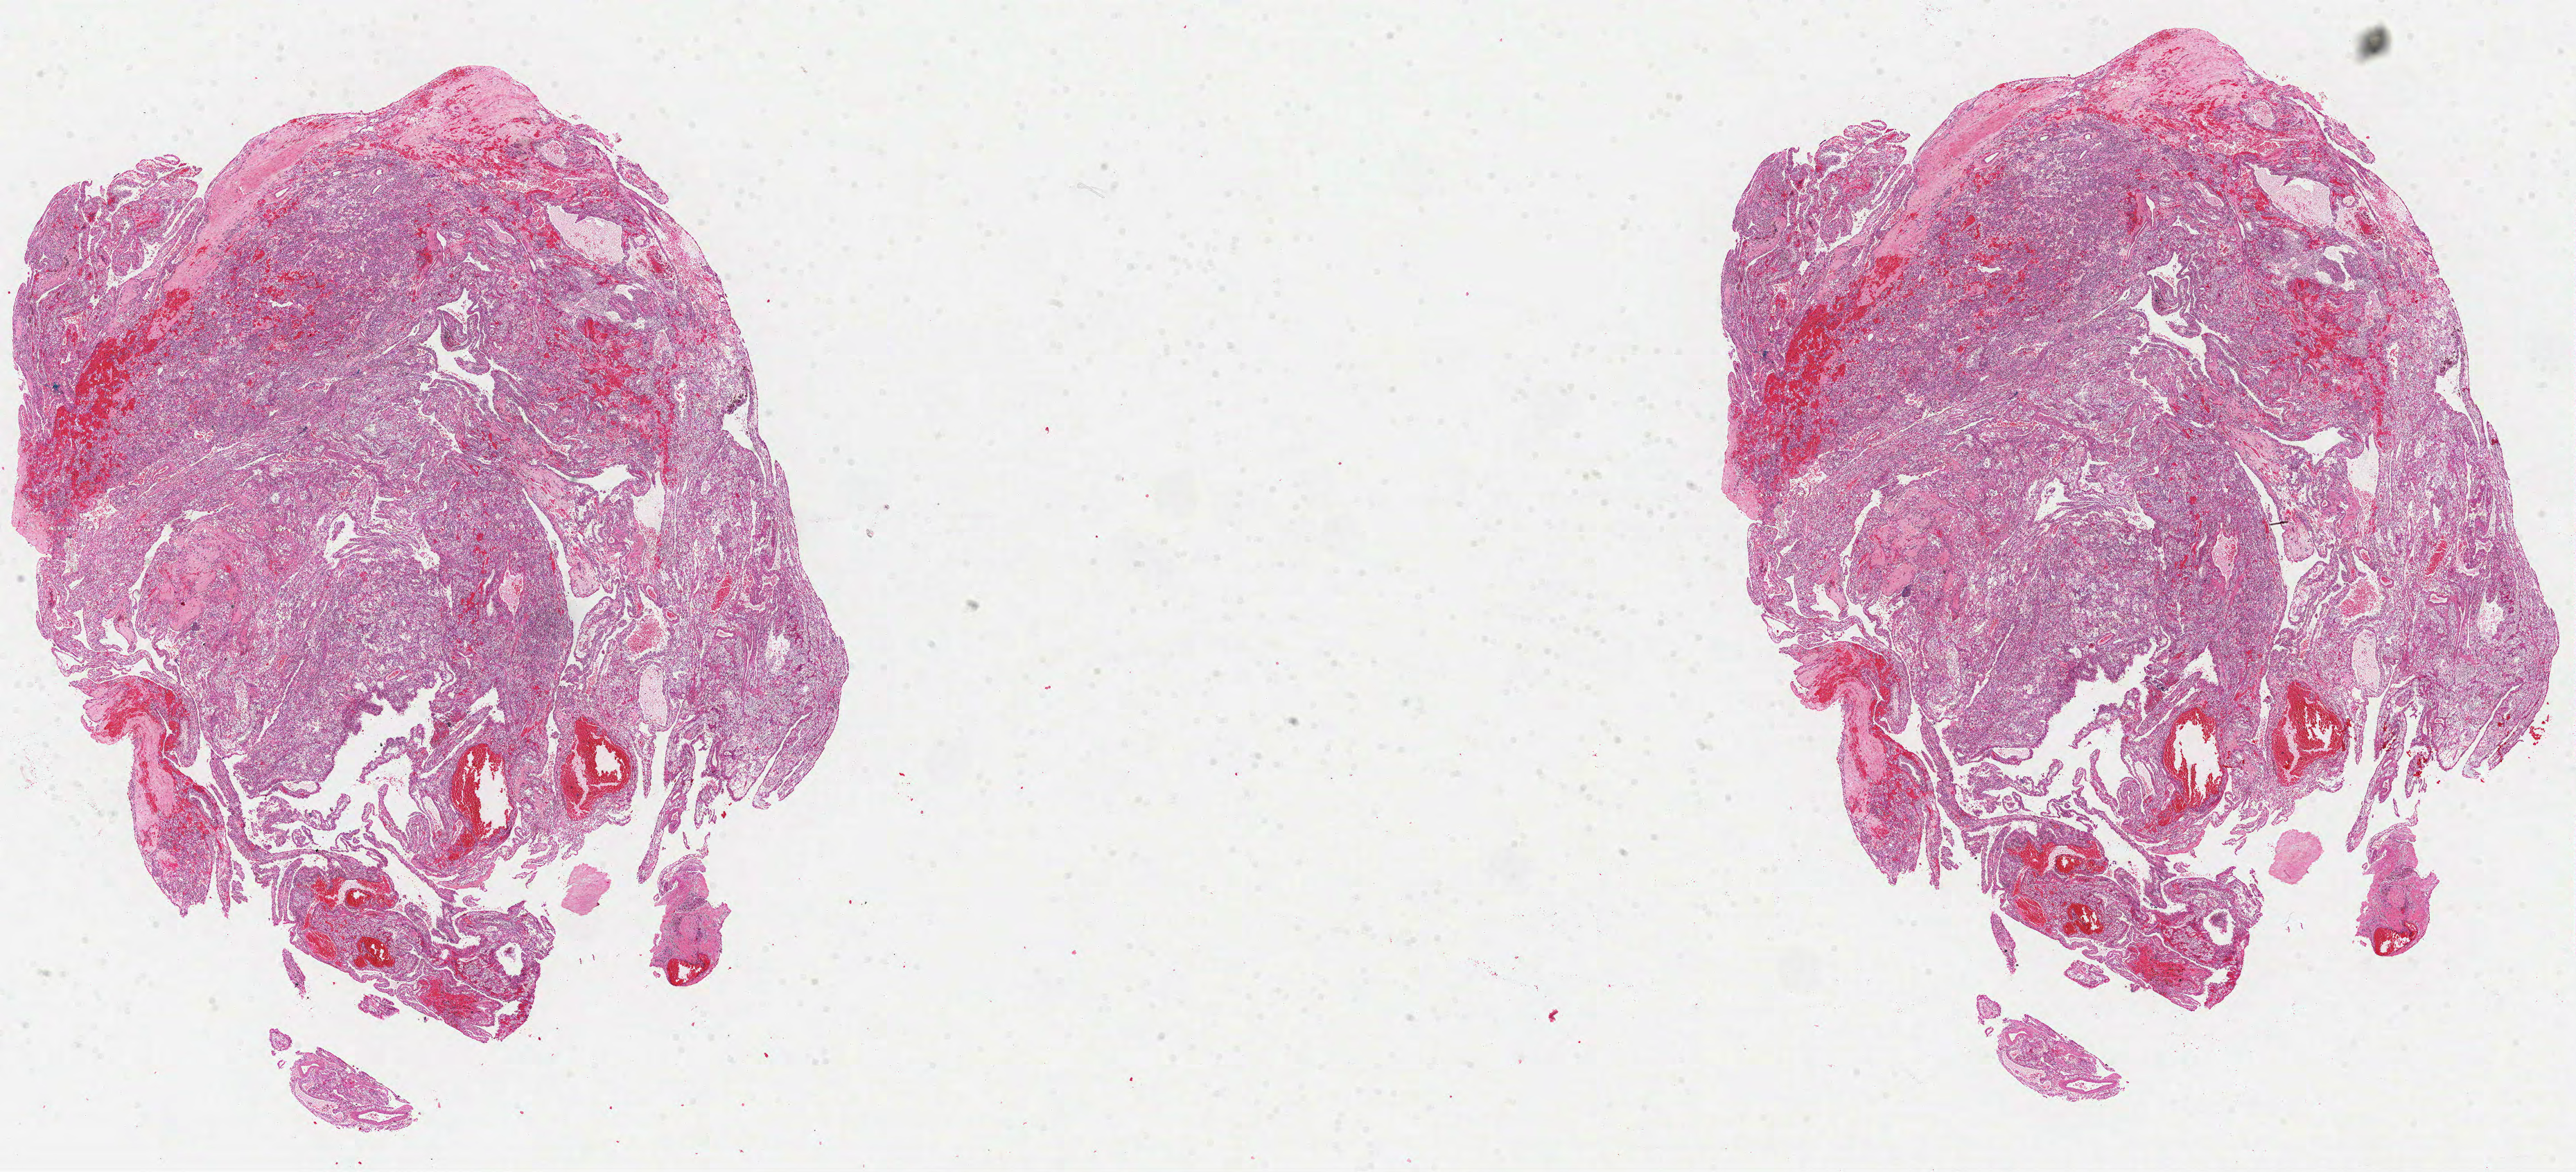
Digitized Hematoxylin and eosin (H&E) stained tissue section (whole slide) — whole scanned area (about 30.0 x 13.6 mm, from a 40x scan) shown as a low-resolution overview, formalin-fixed paraffin-embedded (FFPE) diagnostic section, sample: primary tumour, kidney. Patient: female, age at initial diagnosis 41 years. Histologic grade: G2 (moderately differentiated).
Laterality: right. Diagnosis: Clear cell adenocarcinoma, NOS. AJCC pathologic stage: I.